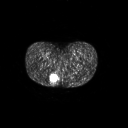
FDG PET of an extremity soft-tissue mass (from a PET/CT study), one axial slice. Position 18 of 267 along the scan axis. 3.27 mm slice thickness. 128 × 128 image matrix. Female patient, age 17 years. Case-level facts recorded for this patient, not image findings: histological type: epithelioid sarcoma; grade: intermediate; site of the primary tumour: right buttock.
Outlined on this slice (expert contour drawn on MRI and transferred to this co-registered scan by the dataset authors):
- gross tumour volume including surrounding oedema: box from (x=49, y=73) to (x=60, y=87) px
- gross tumour volume (mass): (x=51, y=75)–(x=57, y=81)